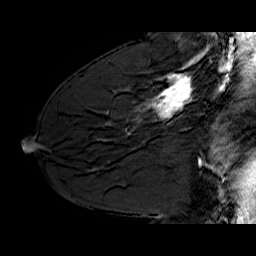
Breast MRI (dynamic contrast-enhanced), one sagittal slice; position 38 of 60 along the scan axis; dynamic contrast-enhanced series, time point 2 of 6 at this slice position (early post-contrast); 1.5 T; TE 6.4 ms, TR 32.9 ms; 256 × 256 image matrix. Female patient. From the clinical record (not read from this slice): setting: breast cancer imaged before/during neoadjuvant chemotherapy; receptor status: HER2-positive.
Annotated regions visible in this slice (semi-automatic segmentation, software-assisted and operator-edited):
- analysis volume of interest (the breast-tissue region the enhancement analysis was run in; not a lesion): bounding box (x1, y1, x2, y2) in pixels: (130, 62, 210, 128)
- tumour enhancement mask (voxels above the 100 % enhancement threshold inside the analysis volume of interest): (148, 62, 193, 119)